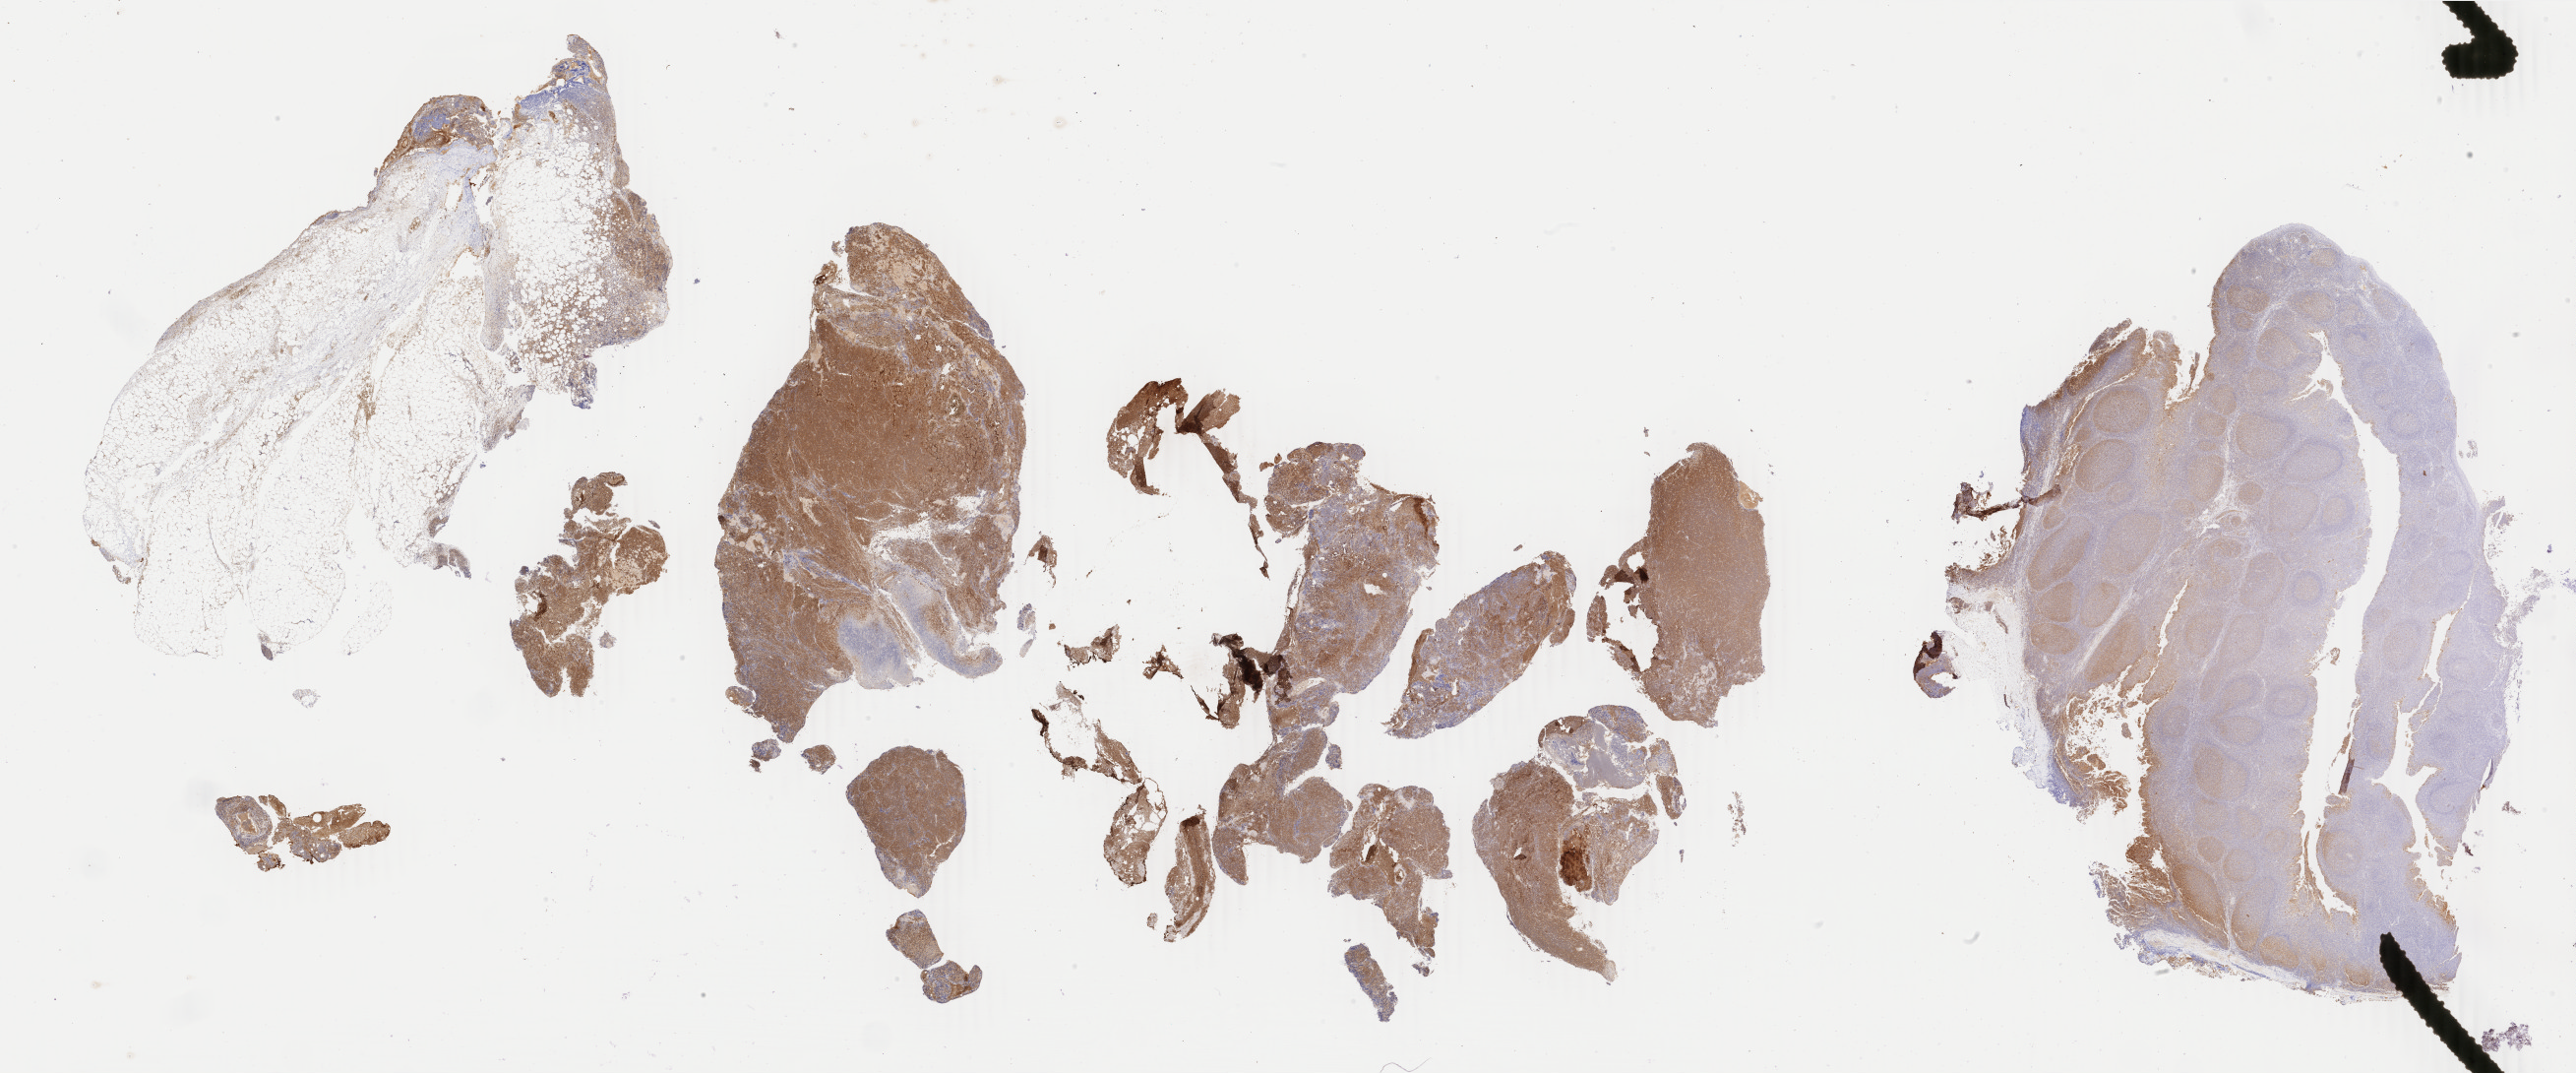
Whole-slide image, immunohistochemical stain for BCL6 — whole scanned area (about 41.6 x 17.3 mm) shown as a low-resolution overview. Tumor tissue. Anatomic site: abdominal lymph node. Male patient, aged 27.
• histologic diagnosis: Burkitt lymphoma, NOS